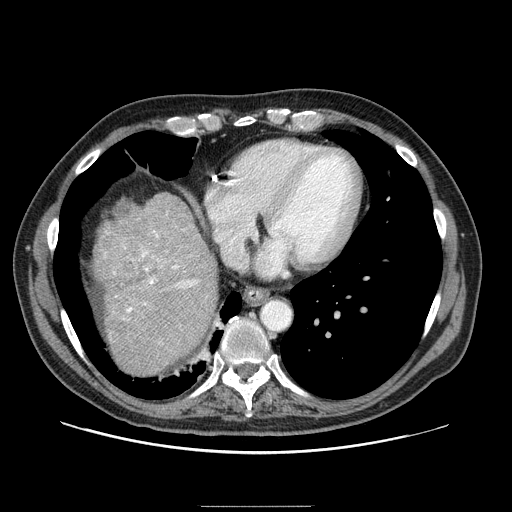
Contrast-enhanced abdominal CT (liver protocol), one axial slice. Position 80 of 99 along the scan axis. Reconstruction kernel STANDARD. One of 2 acquisitions stored at this slice position. Soft-tissue window (W 400 / L 40 HU). 2.5 mm slice thickness. 512 × 512 image matrix, field of view 400 × 400 mm. Case-level facts recorded for this patient, not image findings: diagnosis: hepatocellular carcinoma (patient treated with transarterial chemoembolisation; whether this scan precedes or follows treatment is not stated here); TNM stage (as recorded): Stage-II; Child-Pugh class: A; tumour differentiation: well differentiated; tumour nodularity: multinodular.
Outlined on this slice (semi-automatically segmented with operator editing):
- liver parenchyma outside the tumour (the mass and vessels are separate outlines, so this box may not span the whole liver): box from (x=94, y=194) to (x=216, y=374) px
- liver vessels: (x=113, y=231)–(x=199, y=319)